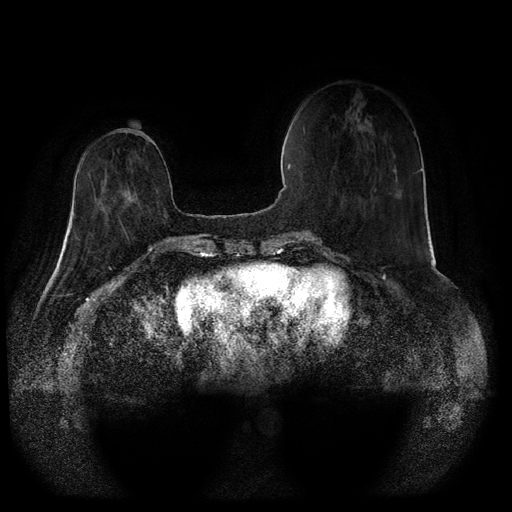
Breast MRI (dynamic contrast-enhanced, multi-phase), one axial slice; slice 24 of 116 in the series (ordered by position); dynamic contrast-enhanced series, time point 2 of 5 at this slice position (early post-contrast); 1.5 T; TE 2.6 ms, TR 5.3 ms; 2 mm slice thickness; 512 × 512 image matrix, field of view 360 × 360 mm. Patient: female, 71 years.
Outlined on this slice (semi-automatic segmentation, software-assisted and operator-edited):
- breast lesion (labelled 'tumour' in the annotation; benign lesions carry a separate 'benign' label): bounding box [x1, y1, x2, y2] px = [123, 189, 132, 202]